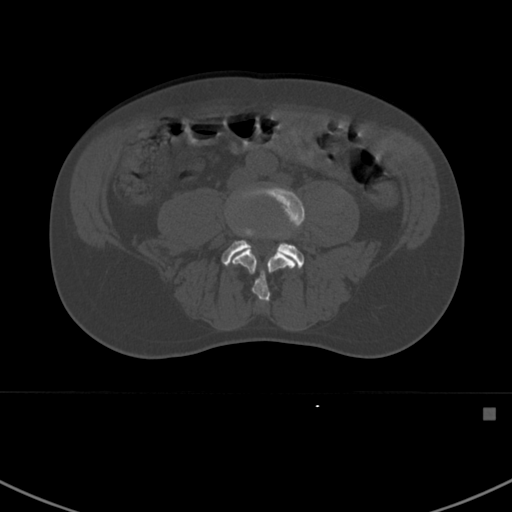
CT including the spine, one axial slice. Slice 232 of 412 in the series (ordered by position). 120 kVp. Bone window (W 1800 / L 400 HU). 1.5 mm slice thickness. 512 × 512 image matrix, field of view 358 × 358 mm. Patient: male, 59 years. From the clinical record (not read from this slice): primary cancer: prostate.
Annotated regions visible in this slice (semi-automatic segmentation, software-assisted and operator-edited):
- L4 vertebra: bounding box <229,186,305,303> (left, top, right, bottom; pixels)
- L5 vertebra: <221,228,304,268>